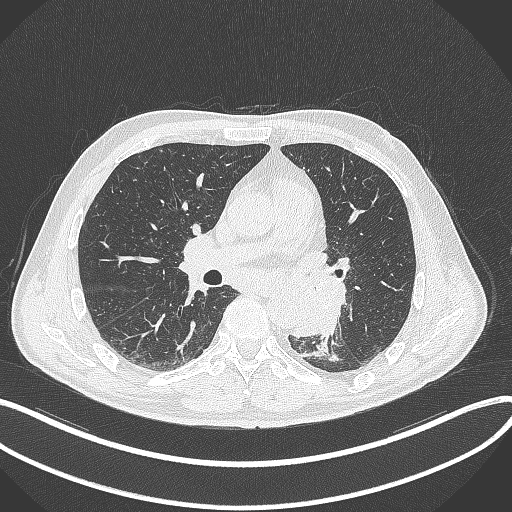
Chest CT, one axial slice. Slice 180 of 329 in the series (ordered by position). Reconstruction kernel B70f. Lung window (W 1500 / L -600 HU). 512 × 512 image matrix, field of view 400 × 400 mm. Male patient, age 59 years. Case-level facts recorded for this patient, not image findings: clinical TNM (as recorded): T2a N2 M0.
Structures marked on this image (rectangle marked by the reading radiologist):
- lung tumour (recorded histology: squamous cell carcinoma): bounding box [x1, y1, x2, y2] px = [283, 271, 347, 338]